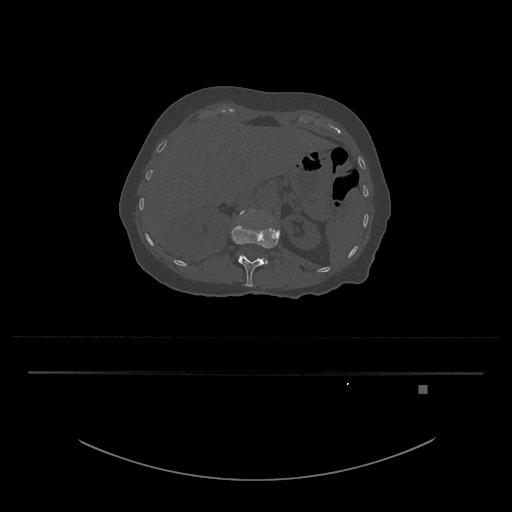
CT including the spine, one axial slice; slice 539 of 797 in the series (ordered by position); reconstruction kernel Br40s/3; 120 kVp; bone window (W 1800 / L 400 HU); 0.5 mm slice thickness; 512 × 512 image matrix. Female patient, age 57 years. Case-level facts recorded for this patient, not image findings: primary cancer: cervical.
Structures marked on this image (semi-automatic segmentation, software-assisted and operator-edited):
- L1 vertebra: bounding box (x1, y1, x2, y2) in pixels: (231, 221, 280, 287)